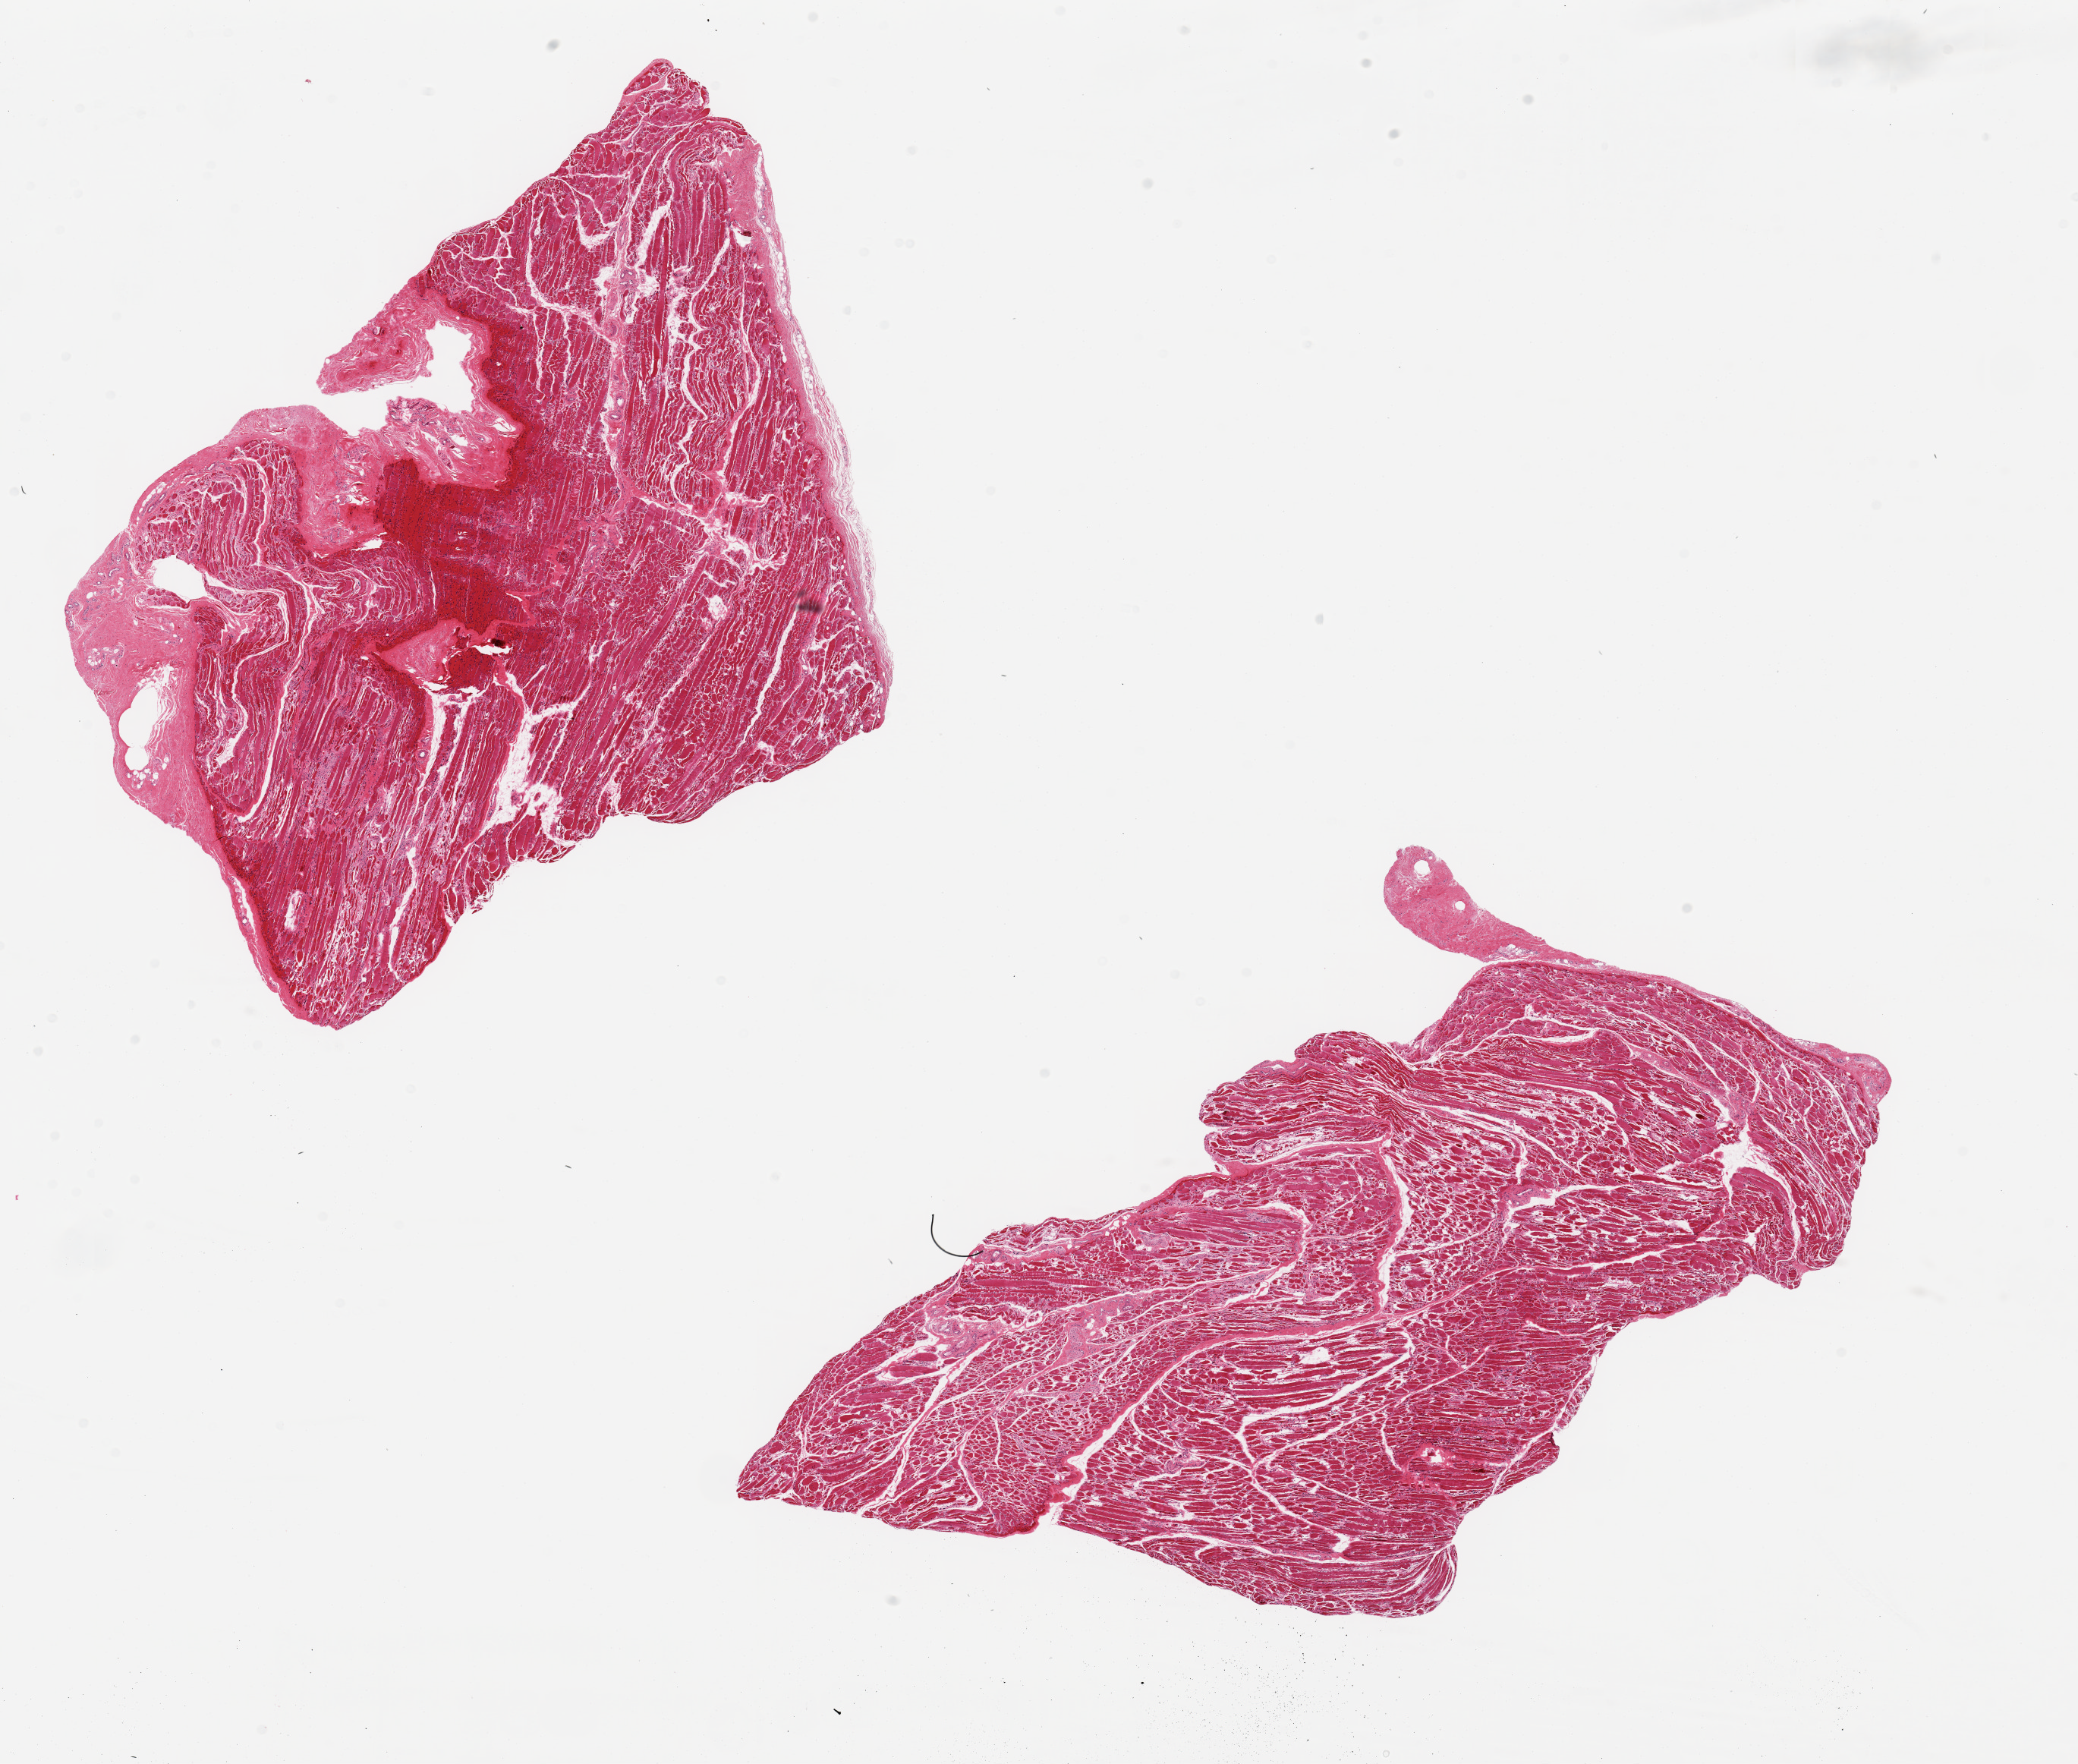
Digitized haematoxylin and eosin-stained section — shown as a low-resolution overview of the whole scanned area (about 21.7 x 18.4 mm, slide scanned at 20x), PAXgene-fixed paraffin-embedded (PFPE) section, section of skeletal muscle (target tissue), donor tissue sample. Donor: female.
Review note (as recorded): 2 pieces, 9x8 & 10x9mm; patchy atrophy (ischemic probably).